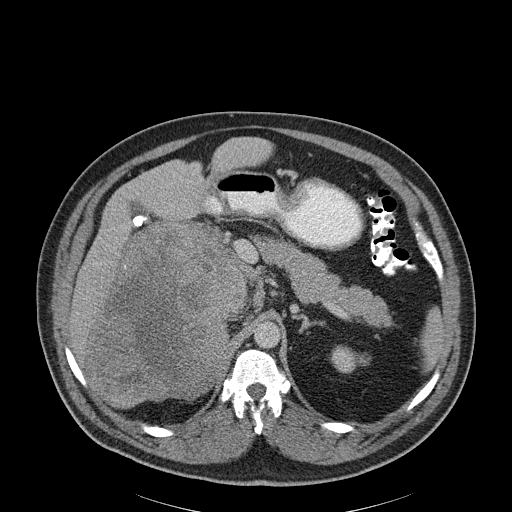
Contrast-enhanced abdominal CT, one axial slice. Slice 135 of 186 in the series (ordered by position). Reconstruction kernel B30f. Soft-tissue window (W 400 / L 40 HU). 3 mm slice thickness. 512 × 512 image matrix, field of view 464 × 464 mm. Patient: male, 56 years. From the clinical record (not read from this slice): diagnosis: adrenocortical carcinoma; tumour side: right adrenal; tumour size at pathology: 18 cm; Ki-67 index: 2 %; stage (as recorded): 3.
Structures marked on this image (semi-automatic segmentation, software-assisted and operator-edited):
- mass: bounding box [x1, y1, x2, y2] px = [89, 225, 244, 407]